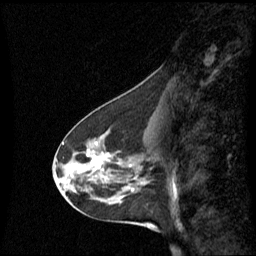
Breast MRI (dynamic contrast-enhanced), one sagittal slice; dynamic contrast-enhanced series, image 2 of 3 at this slice position (ordered by acquisition); 1.5 T; TE 4.2 ms, TR 8.4 ms; 2.2 mm slice thickness; 256 × 256 image matrix, field of view 240 × 240 mm. Patient: female, 45 years. Case-level facts recorded for this patient, not image findings: setting: breast cancer imaged before/during neoadjuvant chemotherapy; receptor status: HR-positive, HER2-negative.
Outlined on this slice (semi-automatically segmented with operator editing):
- analysis volume of interest (the breast-tissue region the enhancement analysis was run in; not a lesion): box from (x=60, y=126) to (x=149, y=215) px
- tumour enhancement mask (voxels above the 70 % enhancement threshold inside the analysis volume of interest): (x=87, y=154)–(x=101, y=169)